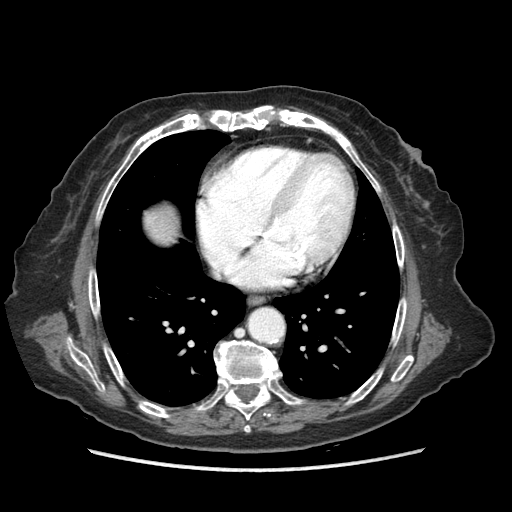
Contrast-enhanced abdominal CT (liver protocol), one axial slice; slice 83 of 89 in the series (ordered by position); reconstruction kernel STANDARD; 140 kVp; soft-tissue window (W 400 / L 40 HU); 2.5 mm slice thickness; 512 × 512 image matrix, field of view 360 × 360 mm. Case-level facts recorded for this patient, not image findings: diagnosis: hepatocellular carcinoma (patient treated with transarterial chemoembolisation; whether this scan precedes or follows treatment is not stated here); TNM stage (as recorded): Stage-IIIA; Child-Pugh class: A; tumour differentiation: well differentiated; tumour nodularity: multinodular.
Annotated regions visible in this slice (semi-automatic segmentation, software-assisted and operator-edited):
- liver parenchyma outside the tumour (the mass and vessels are separate outlines, so this box may not span the whole liver): bounding box <144,206,176,244> (left, top, right, bottom; pixels)